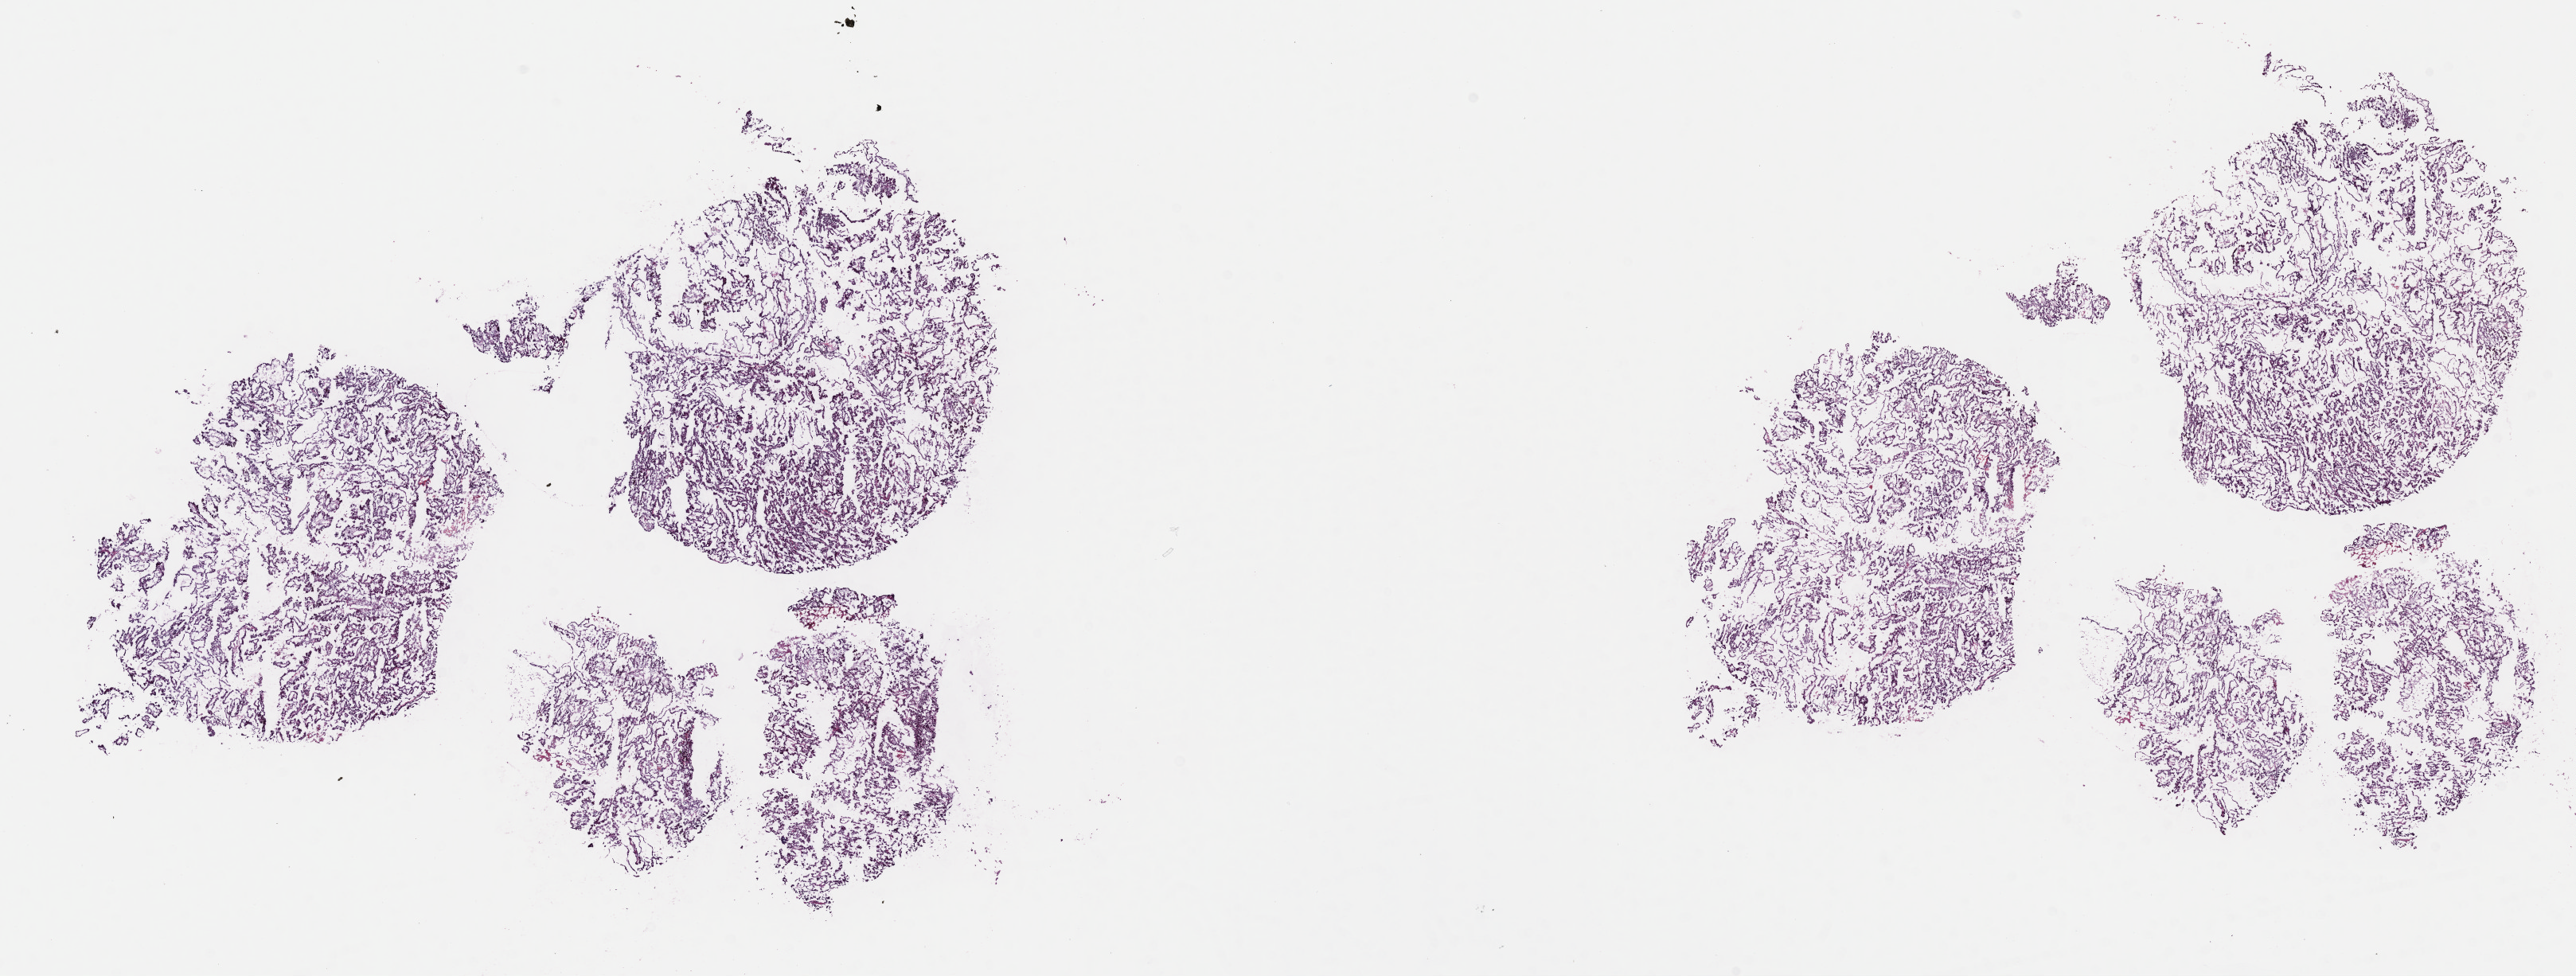
Whole-slide histology image, H&E-stained — shown as a low-resolution overview of the whole scanned area (about 26.2 x 9.9 mm), frozen section from the top of the tissue portion, sample: primary tumour, kidney. Male, age 75 years at initial diagnosis. Composition of this section per pathologist review: tumour cells 100%, tumour nuclei 70%.
Histologic diagnosis: Papillary adenocarcinoma, NOS.